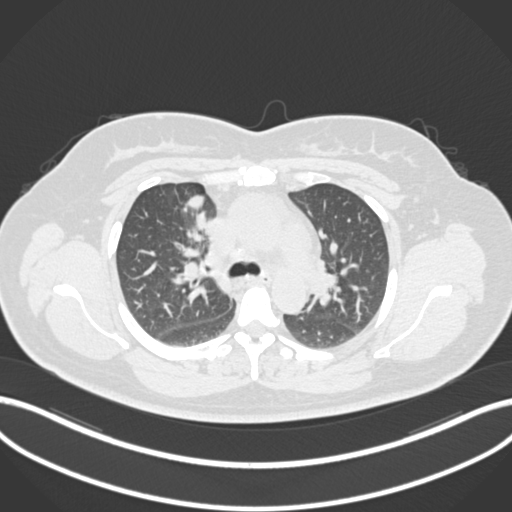
Chest CT, one axial slice; slice 121 of 183 in the series (ordered by position); reconstruction kernel B30f; lung window (W 1500 / L -600 HU); 1 mm slice thickness; 512 × 512 image matrix, field of view 400 × 400 mm. Female patient, age 46 years. Case-level facts recorded for this patient, not image findings: clinical TNM (as recorded): T2a N1 M0.
Outlined on this slice (rectangle marked by the reading radiologist):
- lung tumour (recorded histology: adenocarcinoma): box from (x=184, y=193) to (x=208, y=232) px